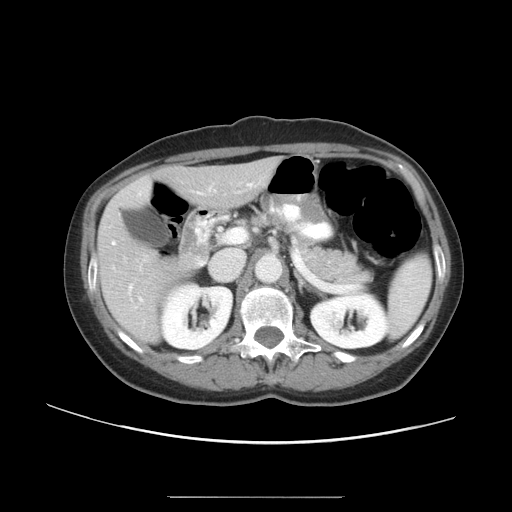
Contrast-enhanced abdominal CT, one axial slice; reconstruction kernel STANDARD; soft-tissue window (W 400 / L 40 HU); 5 mm slice thickness; 512 × 512 image matrix, field of view 389 × 389 mm. Female patient, age 58 years. Case-level facts recorded for this patient, not image findings: diagnosis: colorectal cancer liver metastases, imaged before liver resection; multiple liver metastases: yes; largest metastasis: 7.3 cm; chemotherapy before resection: yes.
Annotated regions visible in this slice (expert manual segmentation):
- hepatic veins: bounding box <112,241,115,245> (left, top, right, bottom; pixels)
- liver: <100,162,274,340>
- planned liver remnant (the part of the liver to remain after resection): <163,162,273,208>
- portal vein (with intrahepatic branches): <140,298,142,301>